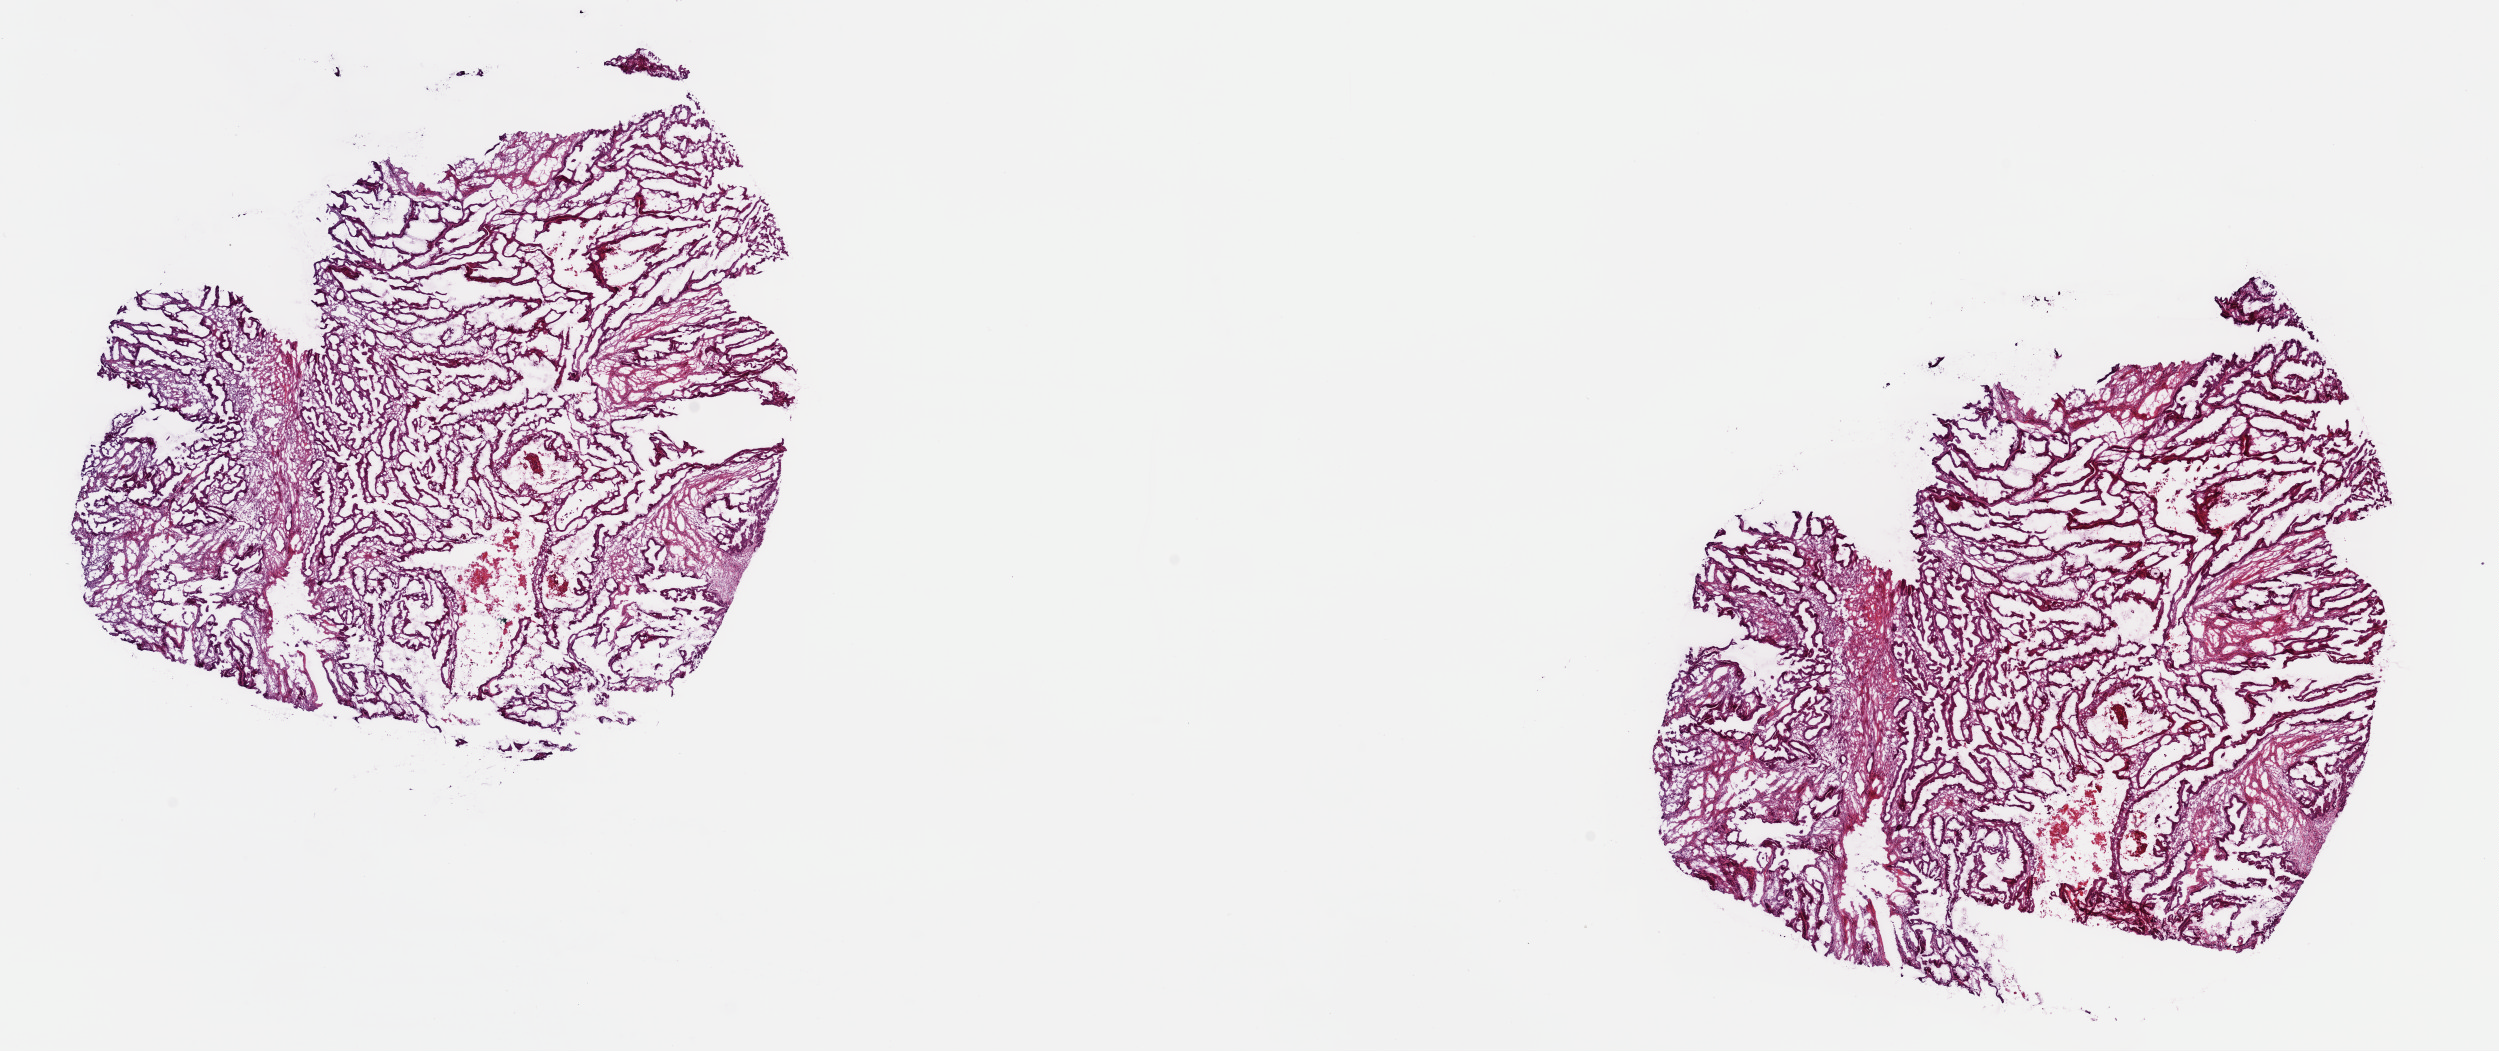
Whole-slide histology image, H&E — a low-resolution overview of the entire scanned area, about 19.7 x 8.3 mm, frozen section, primary tumour sample from the colon. Female patient; age at initial diagnosis 60 years. Composition of this section per pathologist review: tumour cells 64%, tumour nuclei 80%, normal cells 0%, stromal cells 24%, necrosis 12%. Infiltration values recorded for this section: lymphocyte infiltration 1%, monocyte infiltration 0%, neutrophil infiltration 0%.
AJCC pathologic stage: IIA (6th edition). Histologic diagnosis: Mucinous adenocarcinoma (hepatic flexure of colon). Lymph nodes positive (case pathology): 0 of 16 examined.